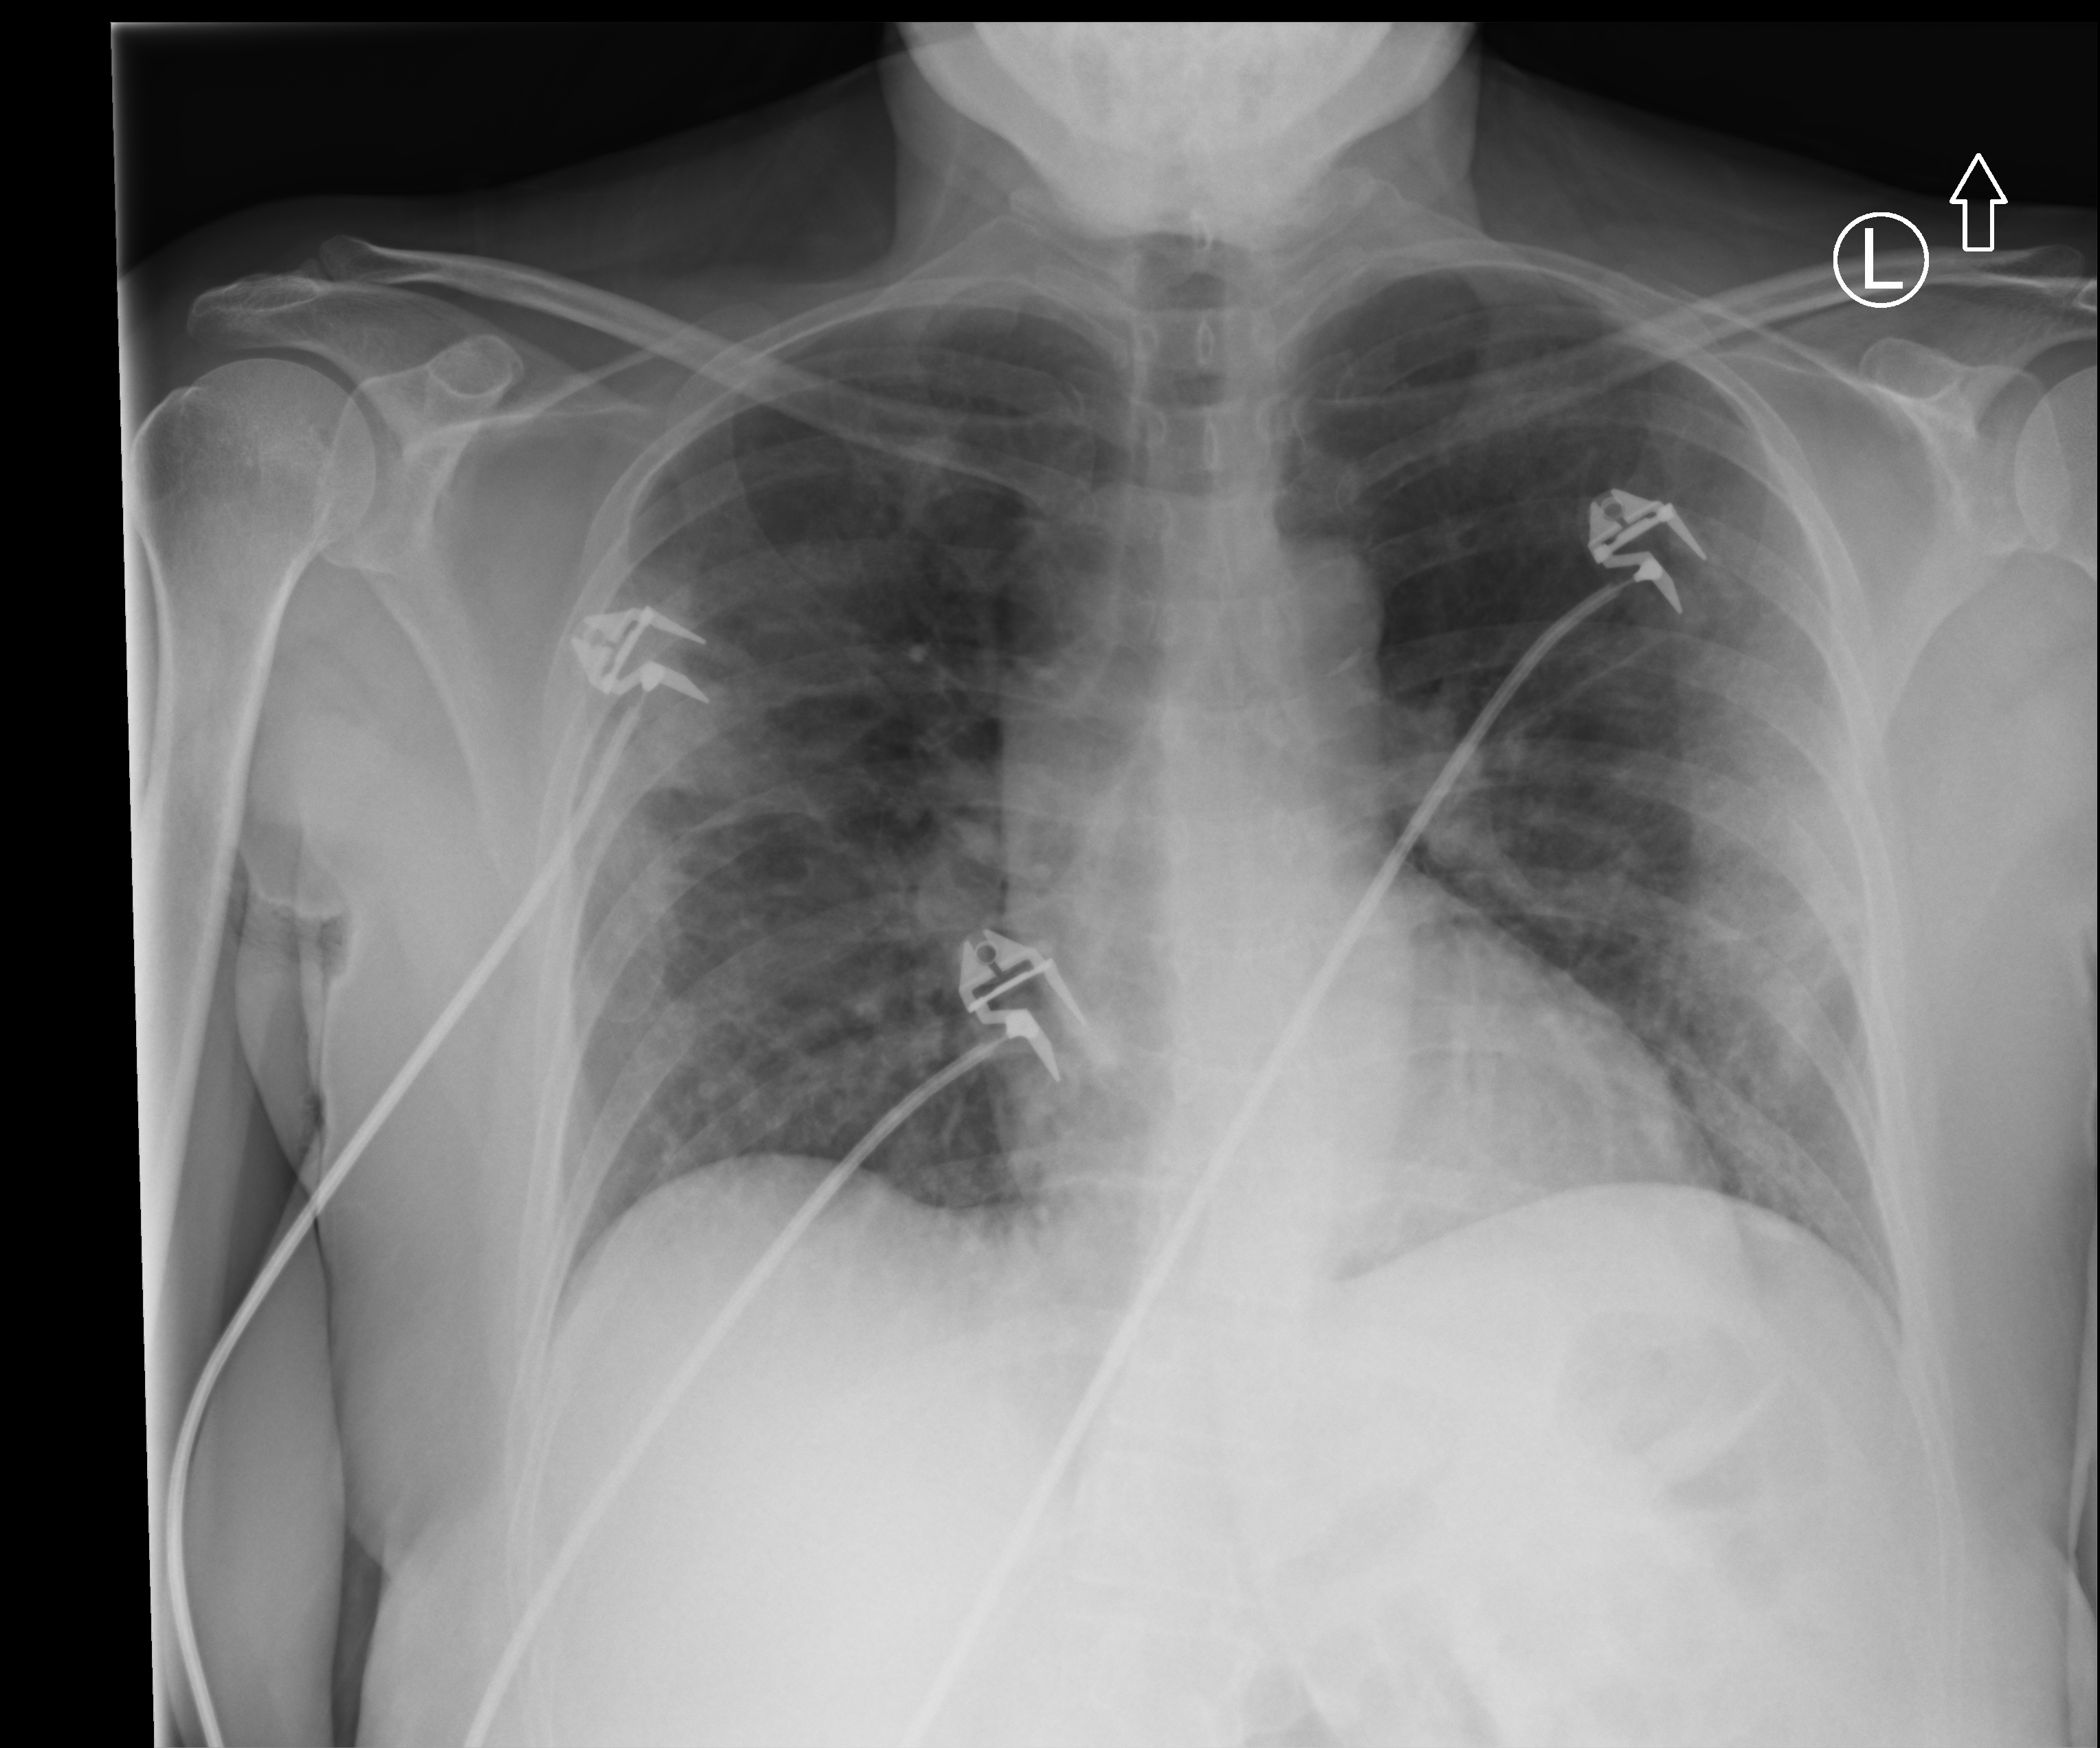
Chest X-ray (portable), anteroposterior (AP) projection. Female patient hospitalised with COVID-19, age 18–59 years.
Hospital-stay facts (about this admission, not read from this image; timing relative to this image not recorded): diabetes (admission record): no.